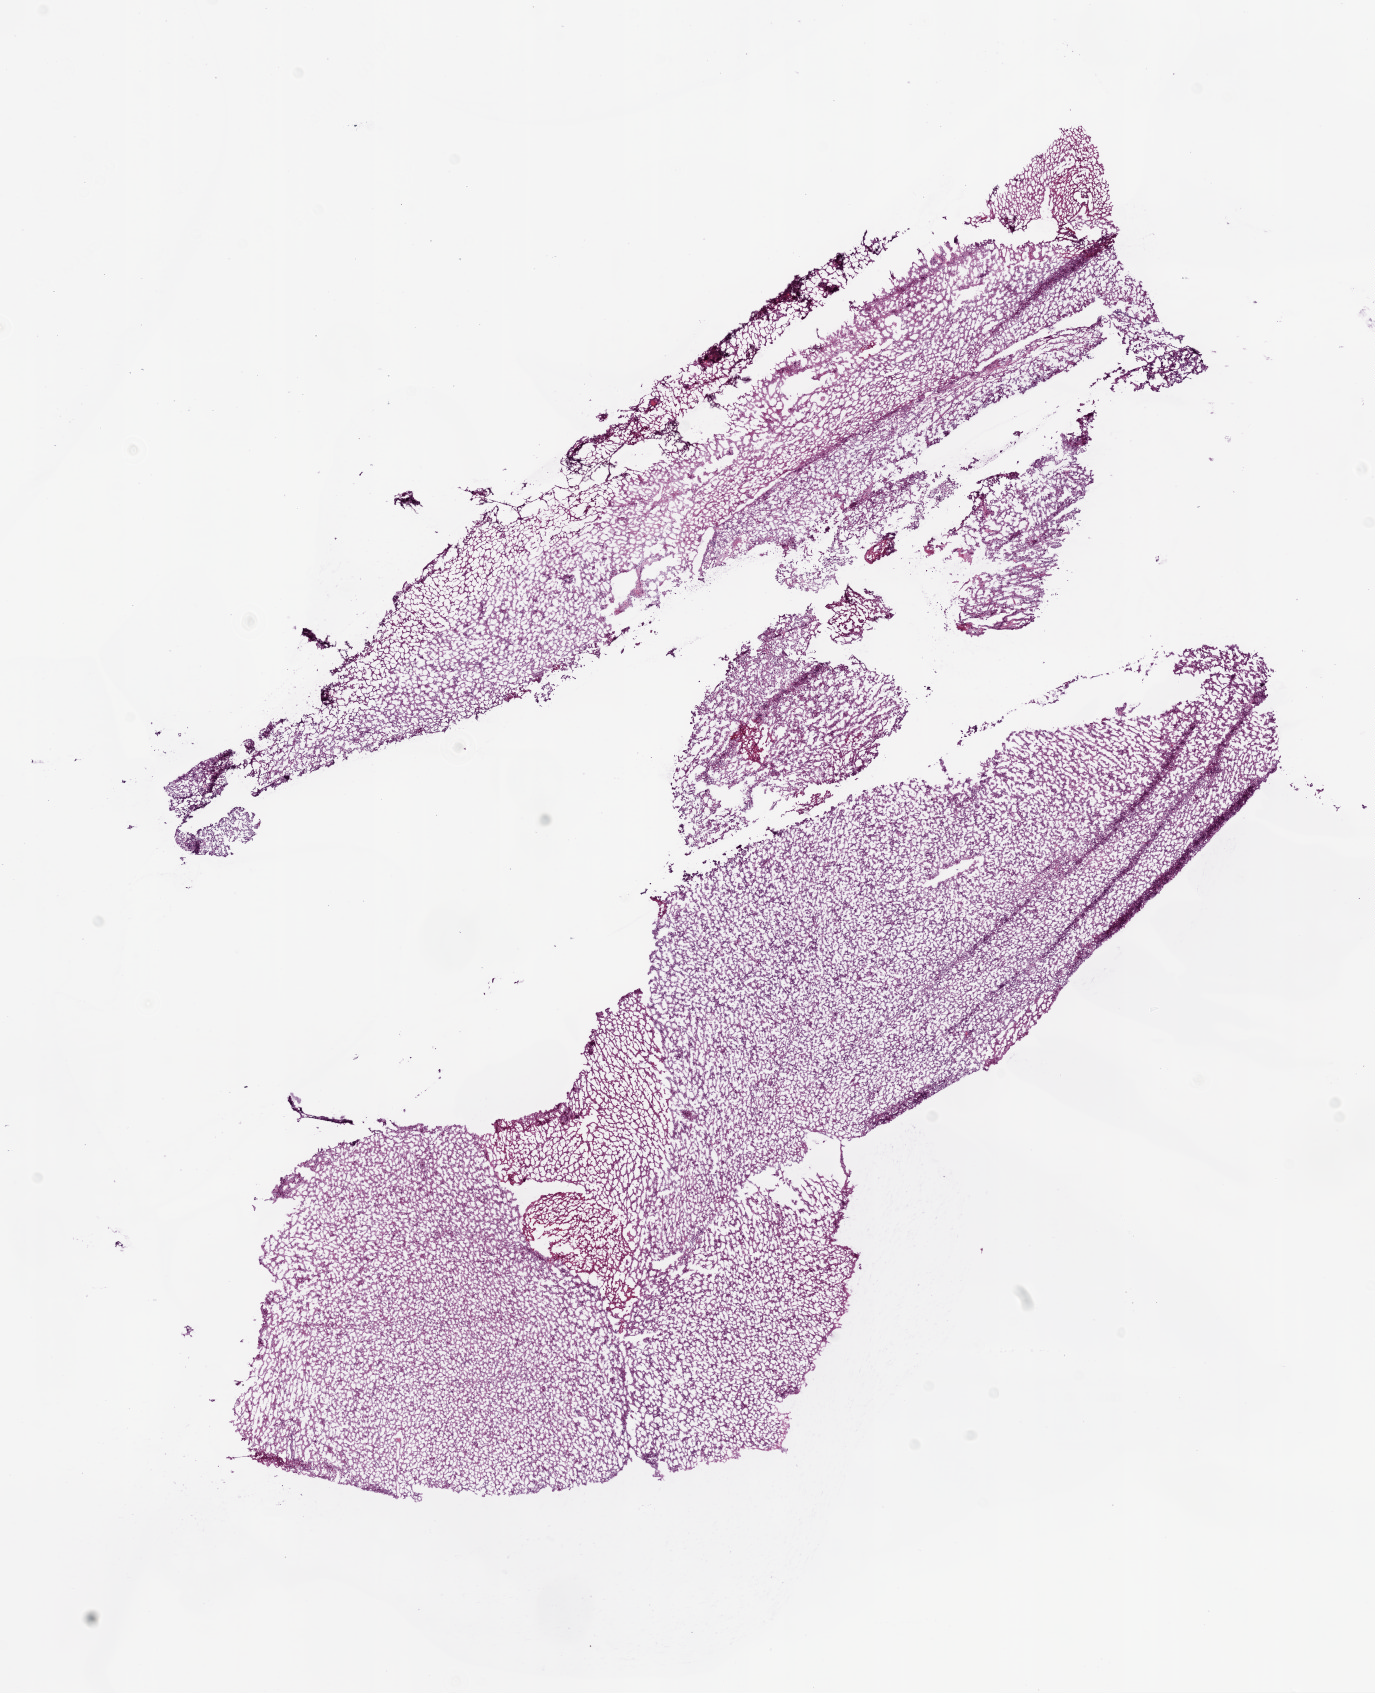
Whole-slide histology image, H&E-stained, whole scanned area (about 11.0 x 13.6 mm, slide scanned at 20x) shown as a low-resolution overview, frozen section from the bottom of the tissue portion, sample: primary tumour, brain. Male, age 66 years at initial diagnosis. Composition of this section per pathologist review: tumour cells 85%, tumour nuclei 95%, normal cells 0%, stromal cells 5%, necrosis 10%.
Pathologic diagnosis: Glioblastoma.